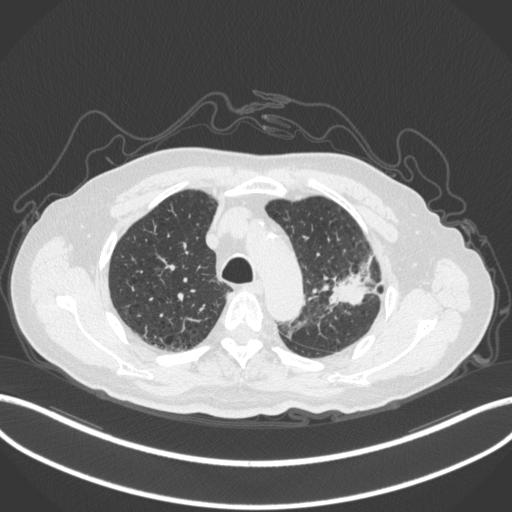
Chest CT, one axial slice. Position 227 of 331 along the scan axis. Reconstruction kernel B31f. 120 kVp. Lung window (W 1500 / L -600 HU). 1 mm slice thickness. 512 × 512 image matrix, field of view 400 × 400 mm. Patient: male, 79 years. From the clinical record (not read from this slice): clinical TNM (as recorded): T2a N1 M1; histopathological grade: G3.
Structures marked on this image (rectangle marked by the reading radiologist):
- lung tumour (recorded histology: adenocarcinoma): box from (x=330, y=257) to (x=384, y=307) px